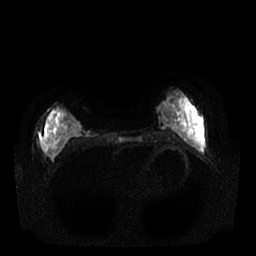
Breast MRI, one axial slice. Diffusion-weighted series; image 2 of 4 stored at this slice position (different b-values; order by instance number). 1.5 T. 256 × 256 image matrix, field of view 340 × 340 mm. Female patient.
Structures marked on this image (manually delineated by an expert):
- tumour on diffusion-weighted imaging: box from (x=41, y=110) to (x=58, y=157) px